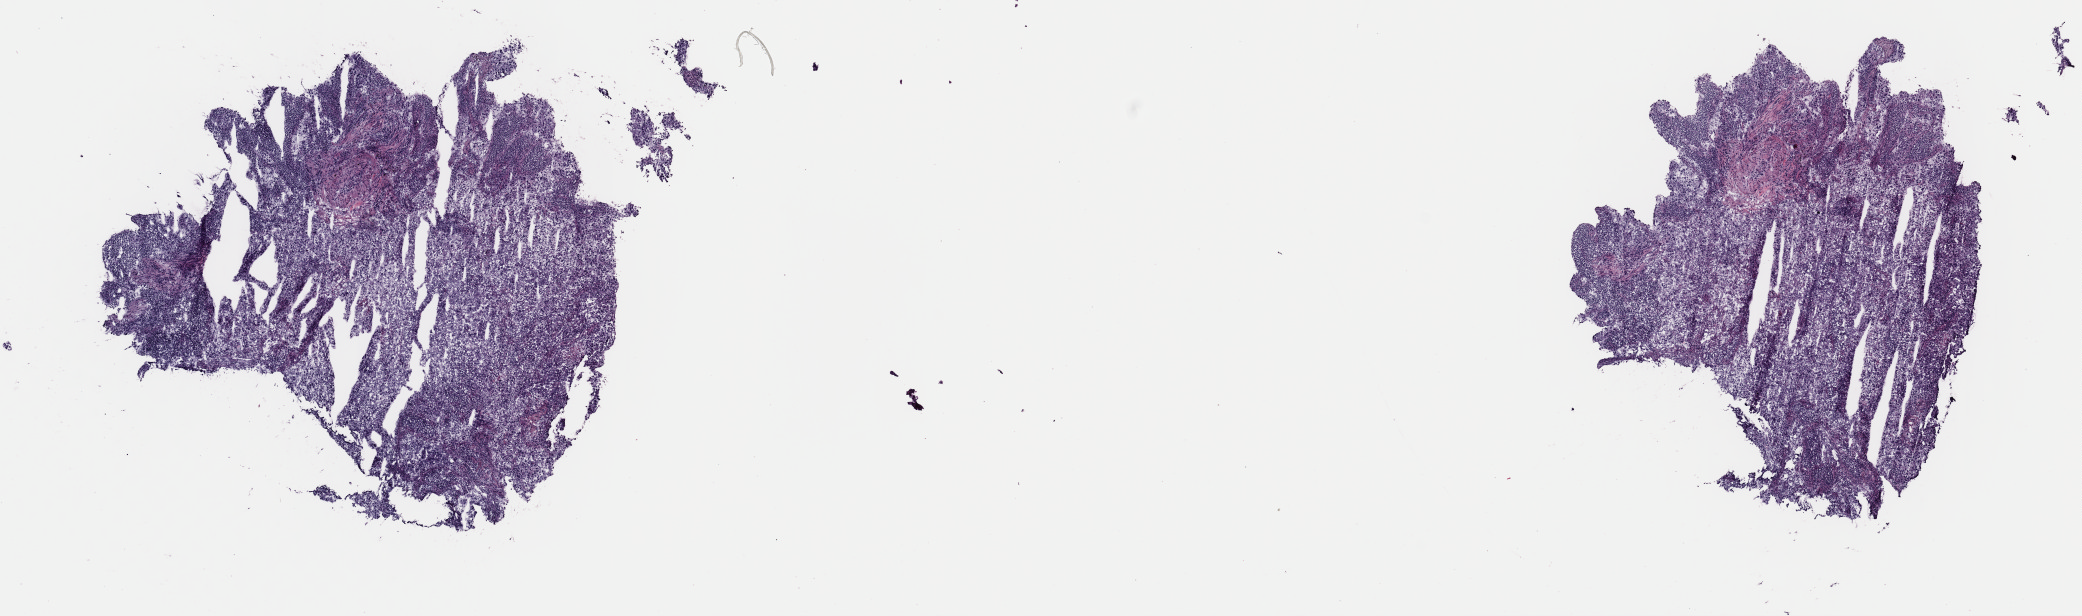
Digitized H&E-stained tissue section (whole slide), a low-resolution overview of the entire scanned area, about 16.4 x 4.9 mm (from a 40x scan), frozen section from the top of the tissue portion, lung, primary tumour sample. Male patient; age at initial diagnosis 59 years. Composition of this section per pathologist review: tumour cells 70%, tumour nuclei 70%, normal cells 0%, stromal cells 30%, necrosis 0%. Inflammatory infiltration, as recorded: lymphocyte infiltration 5%, monocyte infiltration 3%, neutrophil infiltration 3%.
Histologic diagnosis: Adenocarcinoma, NOS (upper lobe, lung). AJCC pathologic stage: IIA. Laterality: right.